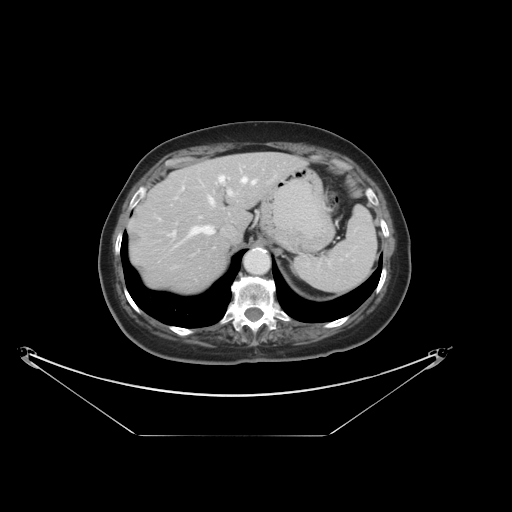
Contrast-enhanced abdominal CT, one axial slice. Slice 27 of 36 in the series (ordered by position). 120 kVp. Soft-tissue window (W 400 / L 40 HU). 5 mm slice thickness. 512 × 512 image matrix, field of view 500 × 500 mm. Female patient, age 70 years. Case-level facts recorded for this patient, not image findings: diagnosis: colorectal cancer liver metastases, imaged before liver resection; multiple liver metastases: no; largest metastasis: 2.5 cm; disease in both lobes: no.
Annotated regions visible in this slice (manually delineated by an expert):
- hepatic veins: box from (x=175, y=176) to (x=256, y=247) px
- liver: (x=129, y=153)–(x=306, y=294)
- planned liver remnant (the part of the liver to remain after resection): (x=129, y=153)–(x=306, y=294)
- portal vein (with intrahepatic branches): (x=167, y=181)–(x=236, y=238)